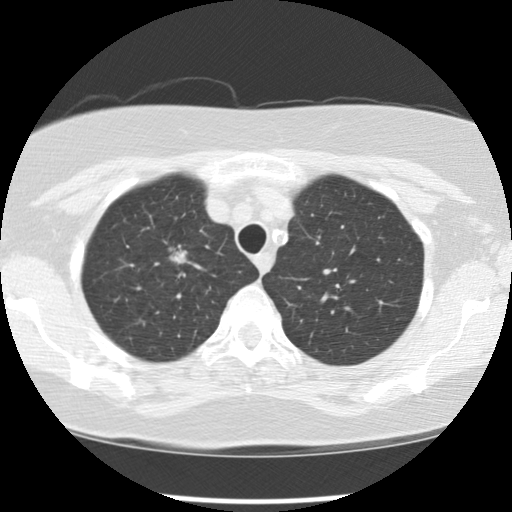
Axial slice from a low-dose chest CT screening exam, baseline annual screen, lung window (W 1500 / L -600 HU), 2.5 mm slice thickness, slice 22 of 113 in the series, 512 × 512 image matrix. Female participant, aged 65 years at enrolment. Current smoker at enrolment.
Lesion marked by an expert reader, bounding box (x1, y1, x2, y2) in pixels: (144, 229, 199, 283). The screening reader recorded 2 non-calcified nodules or masses ≥4 mm on this exam (right upper lobe, right upper lobe); which of them this box marks is not recorded. Lung cancer was diagnosed 183 days after this screen: large cell carcinoma, NOS, right upper lobe, poorly differentiated (G3), stage IA (AJCC 6th edition), 20 mm at pathology.